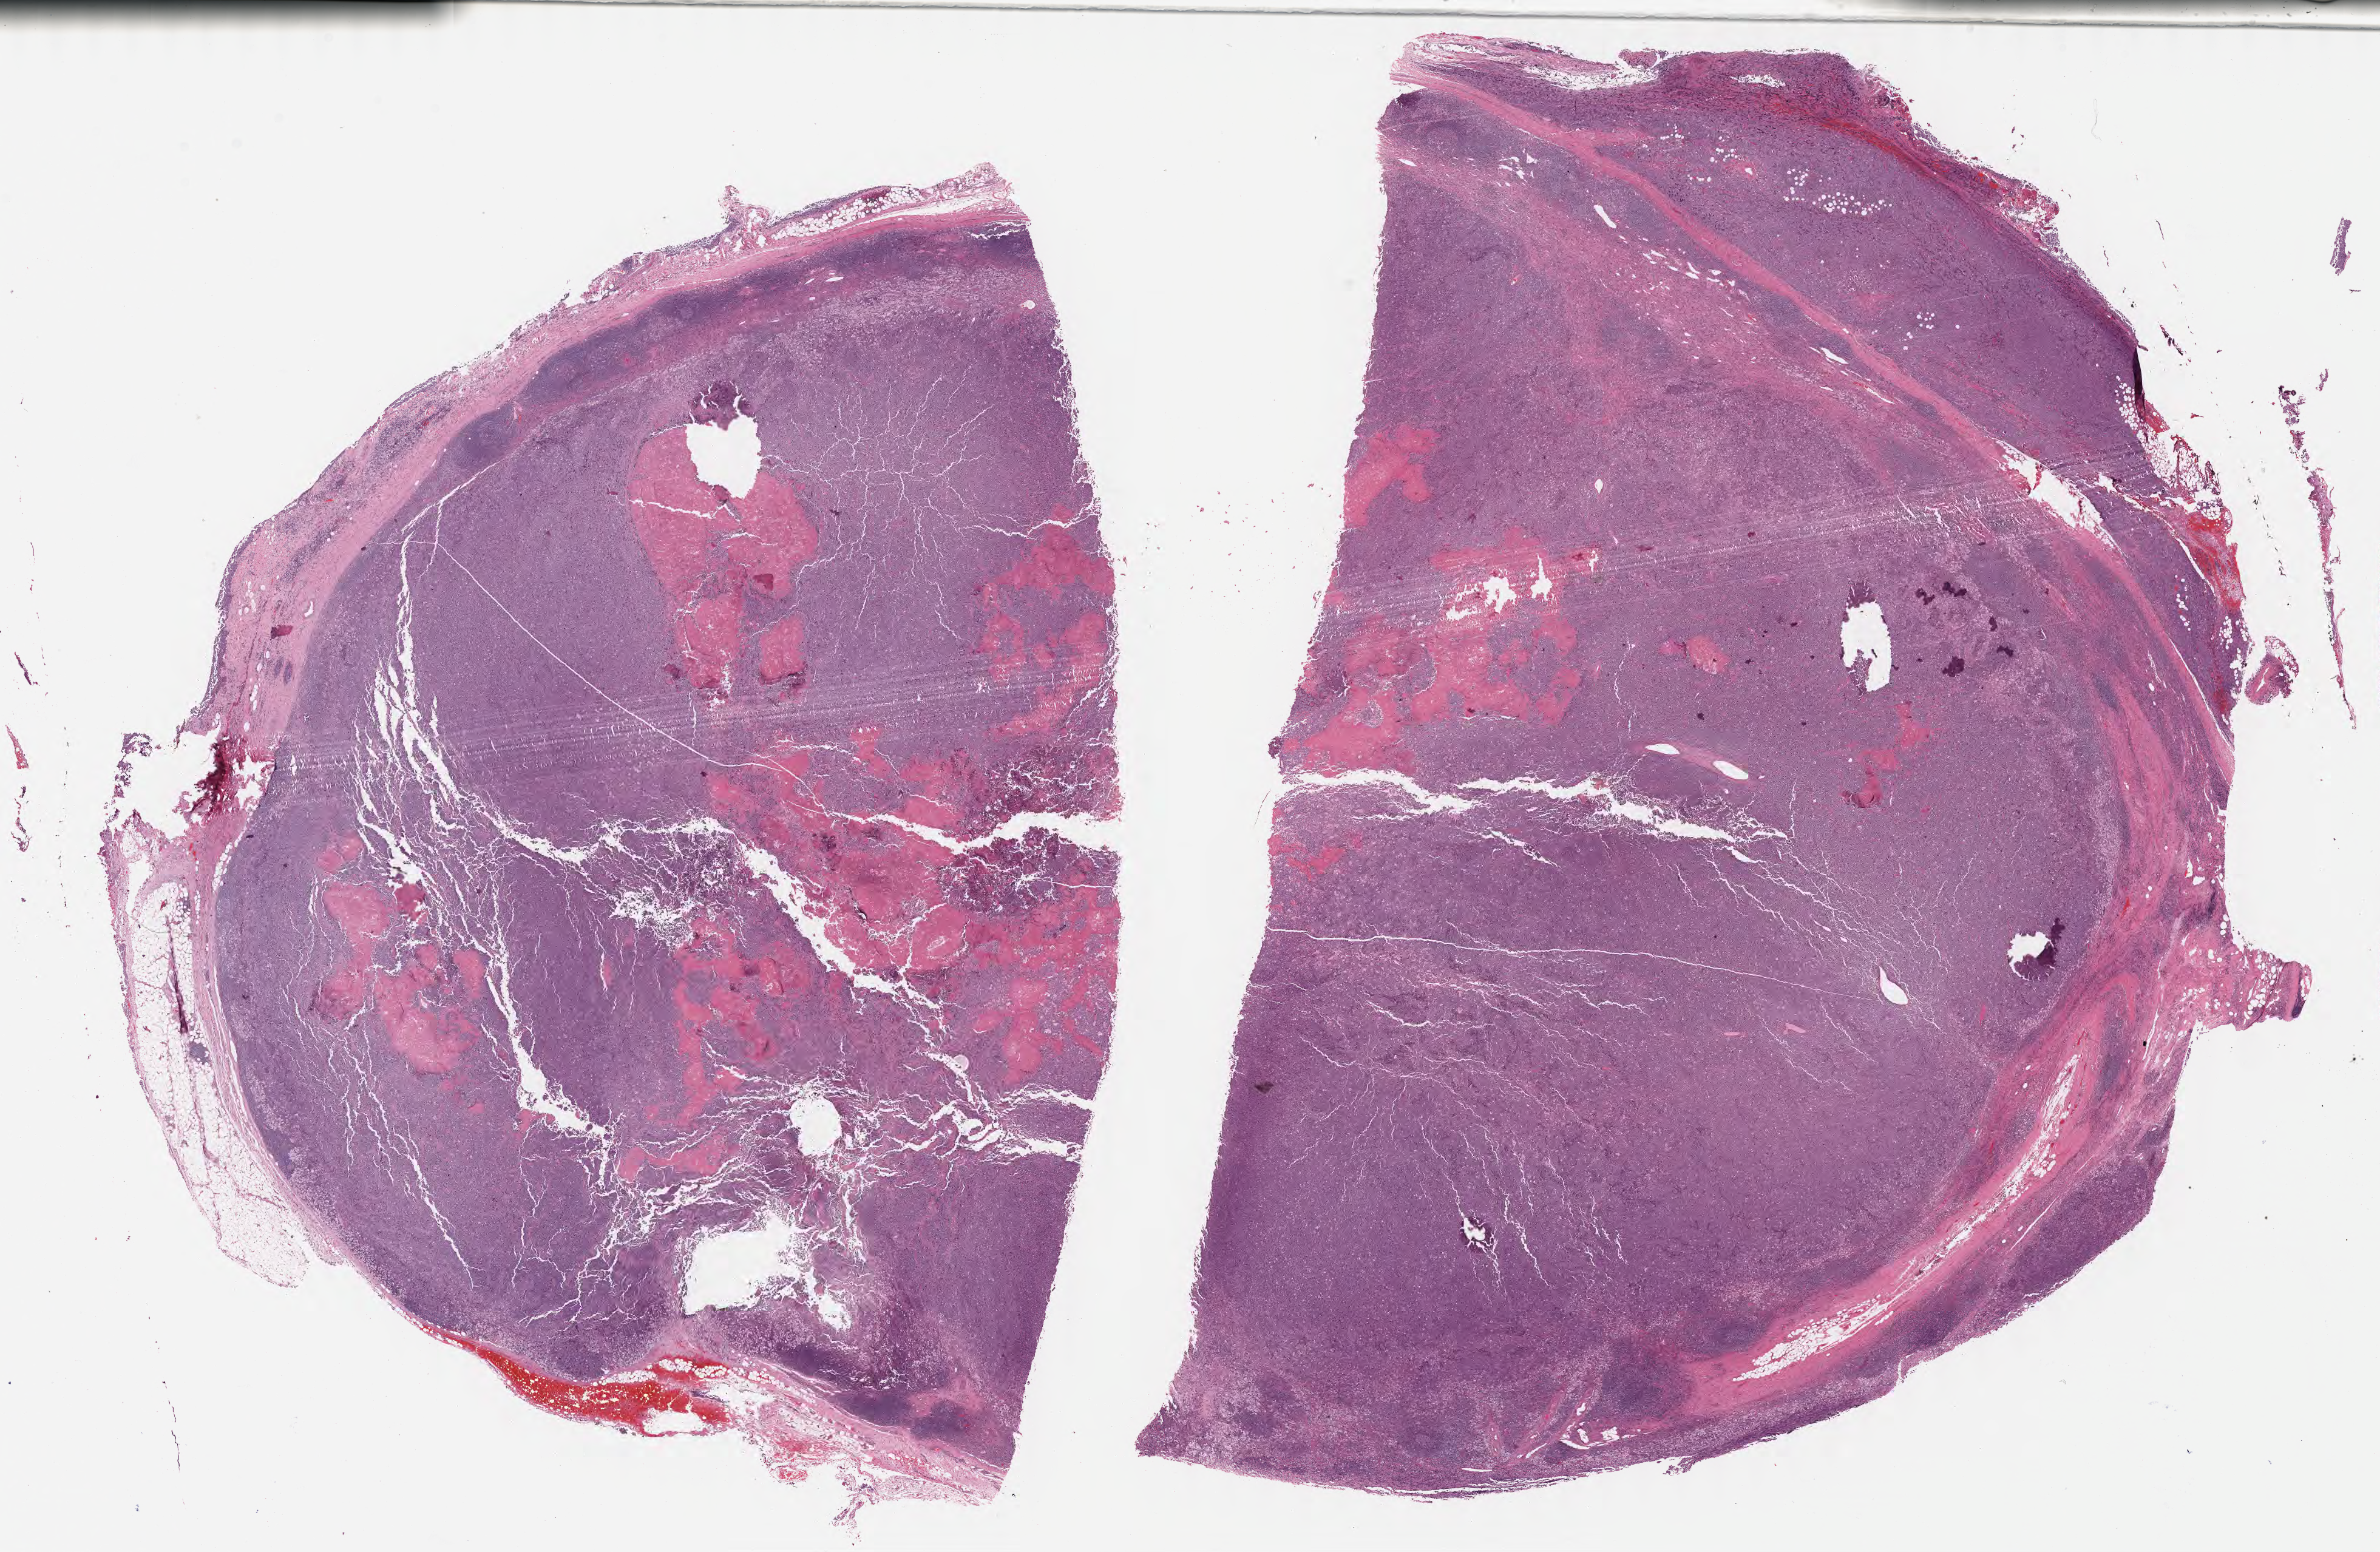
Whole-slide image, H&E stain, shown as a low-resolution overview of the whole scanned area (about 31.7 x 20.7 mm); formalin-fixed, paraffin-embedded (FFPE) tissue; primary tumor. Patient: male, 48 years old. Slide review estimates, as recorded: tumor cells 85%, tumor nuclei 90%, stromal cells 10%, necrosis 5%, normal cells 0%. Infiltration values recorded for this section: lymphocyte infiltration 10%, monocyte infiltration 30%, neutrophil infiltration 10%.
Ann Arbor stage (patient): Stage IV. Section: bottom of the tissue portion. Histologic diagnosis: Burkitt lymphoma, NOS.